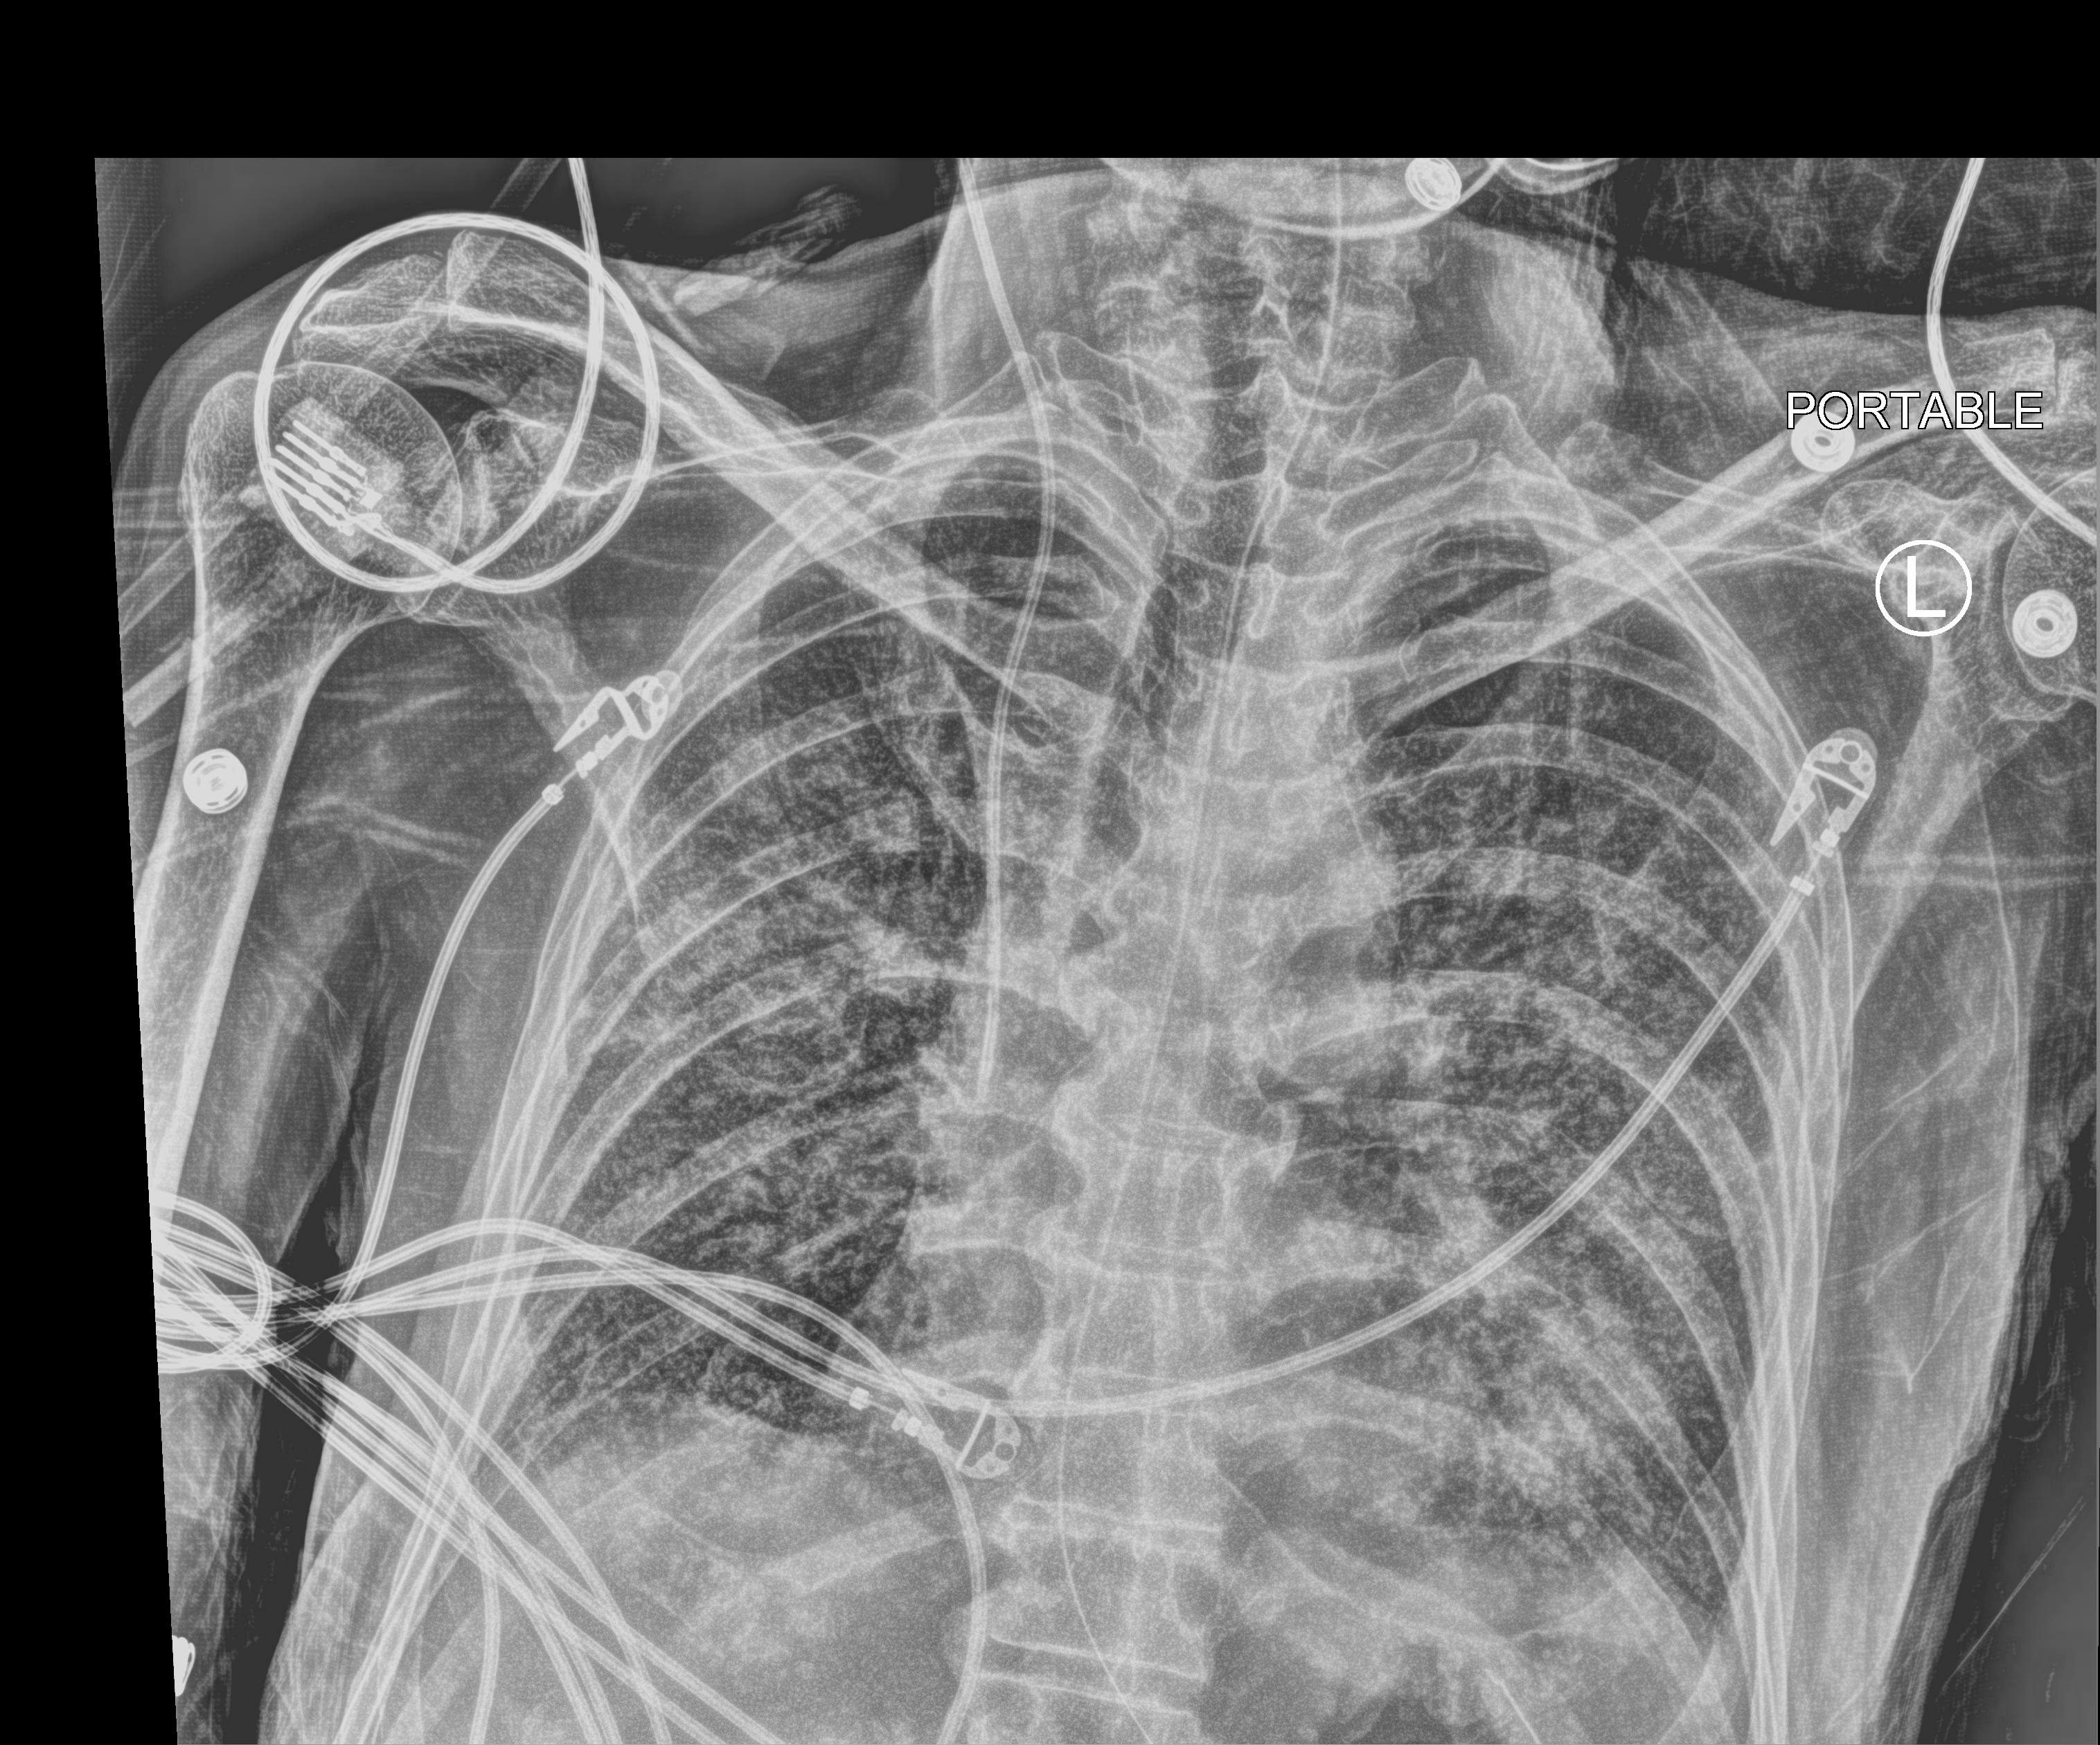
Bedside chest radiograph (computed radiography), anteroposterior (AP) projection. Patient hospitalised with COVID-19; male, aged 60–74 years.
From the hospital-stay record, not from the radiograph (when in the stay this image was taken is not recorded): length of hospital stay: 42 days; smoking status (admission record): current.